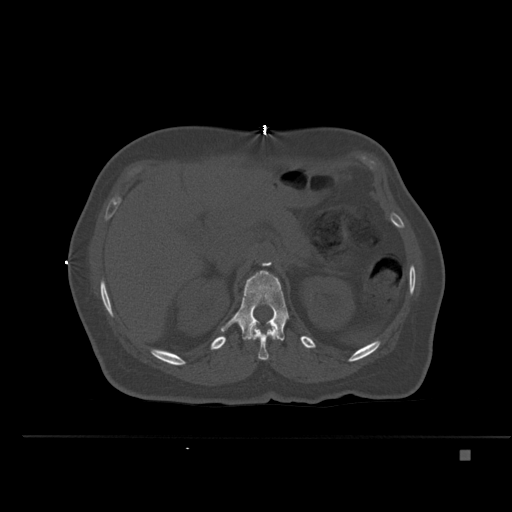
CT including the spine, one axial slice; position 241 of 477 along the scan axis; bone window (W 1800 / L 400 HU); 512 × 512 image matrix, field of view 422 × 422 mm. Female patient, age 74 years. From the clinical record (not read from this slice): primary cancer: colon.
Structures marked on this image (semi-automatic segmentation, software-assisted and operator-edited):
- L1 vertebra: bounding box <221,270,289,341> (left, top, right, bottom; pixels)
- T12 vertebra: <250,325,277,360>